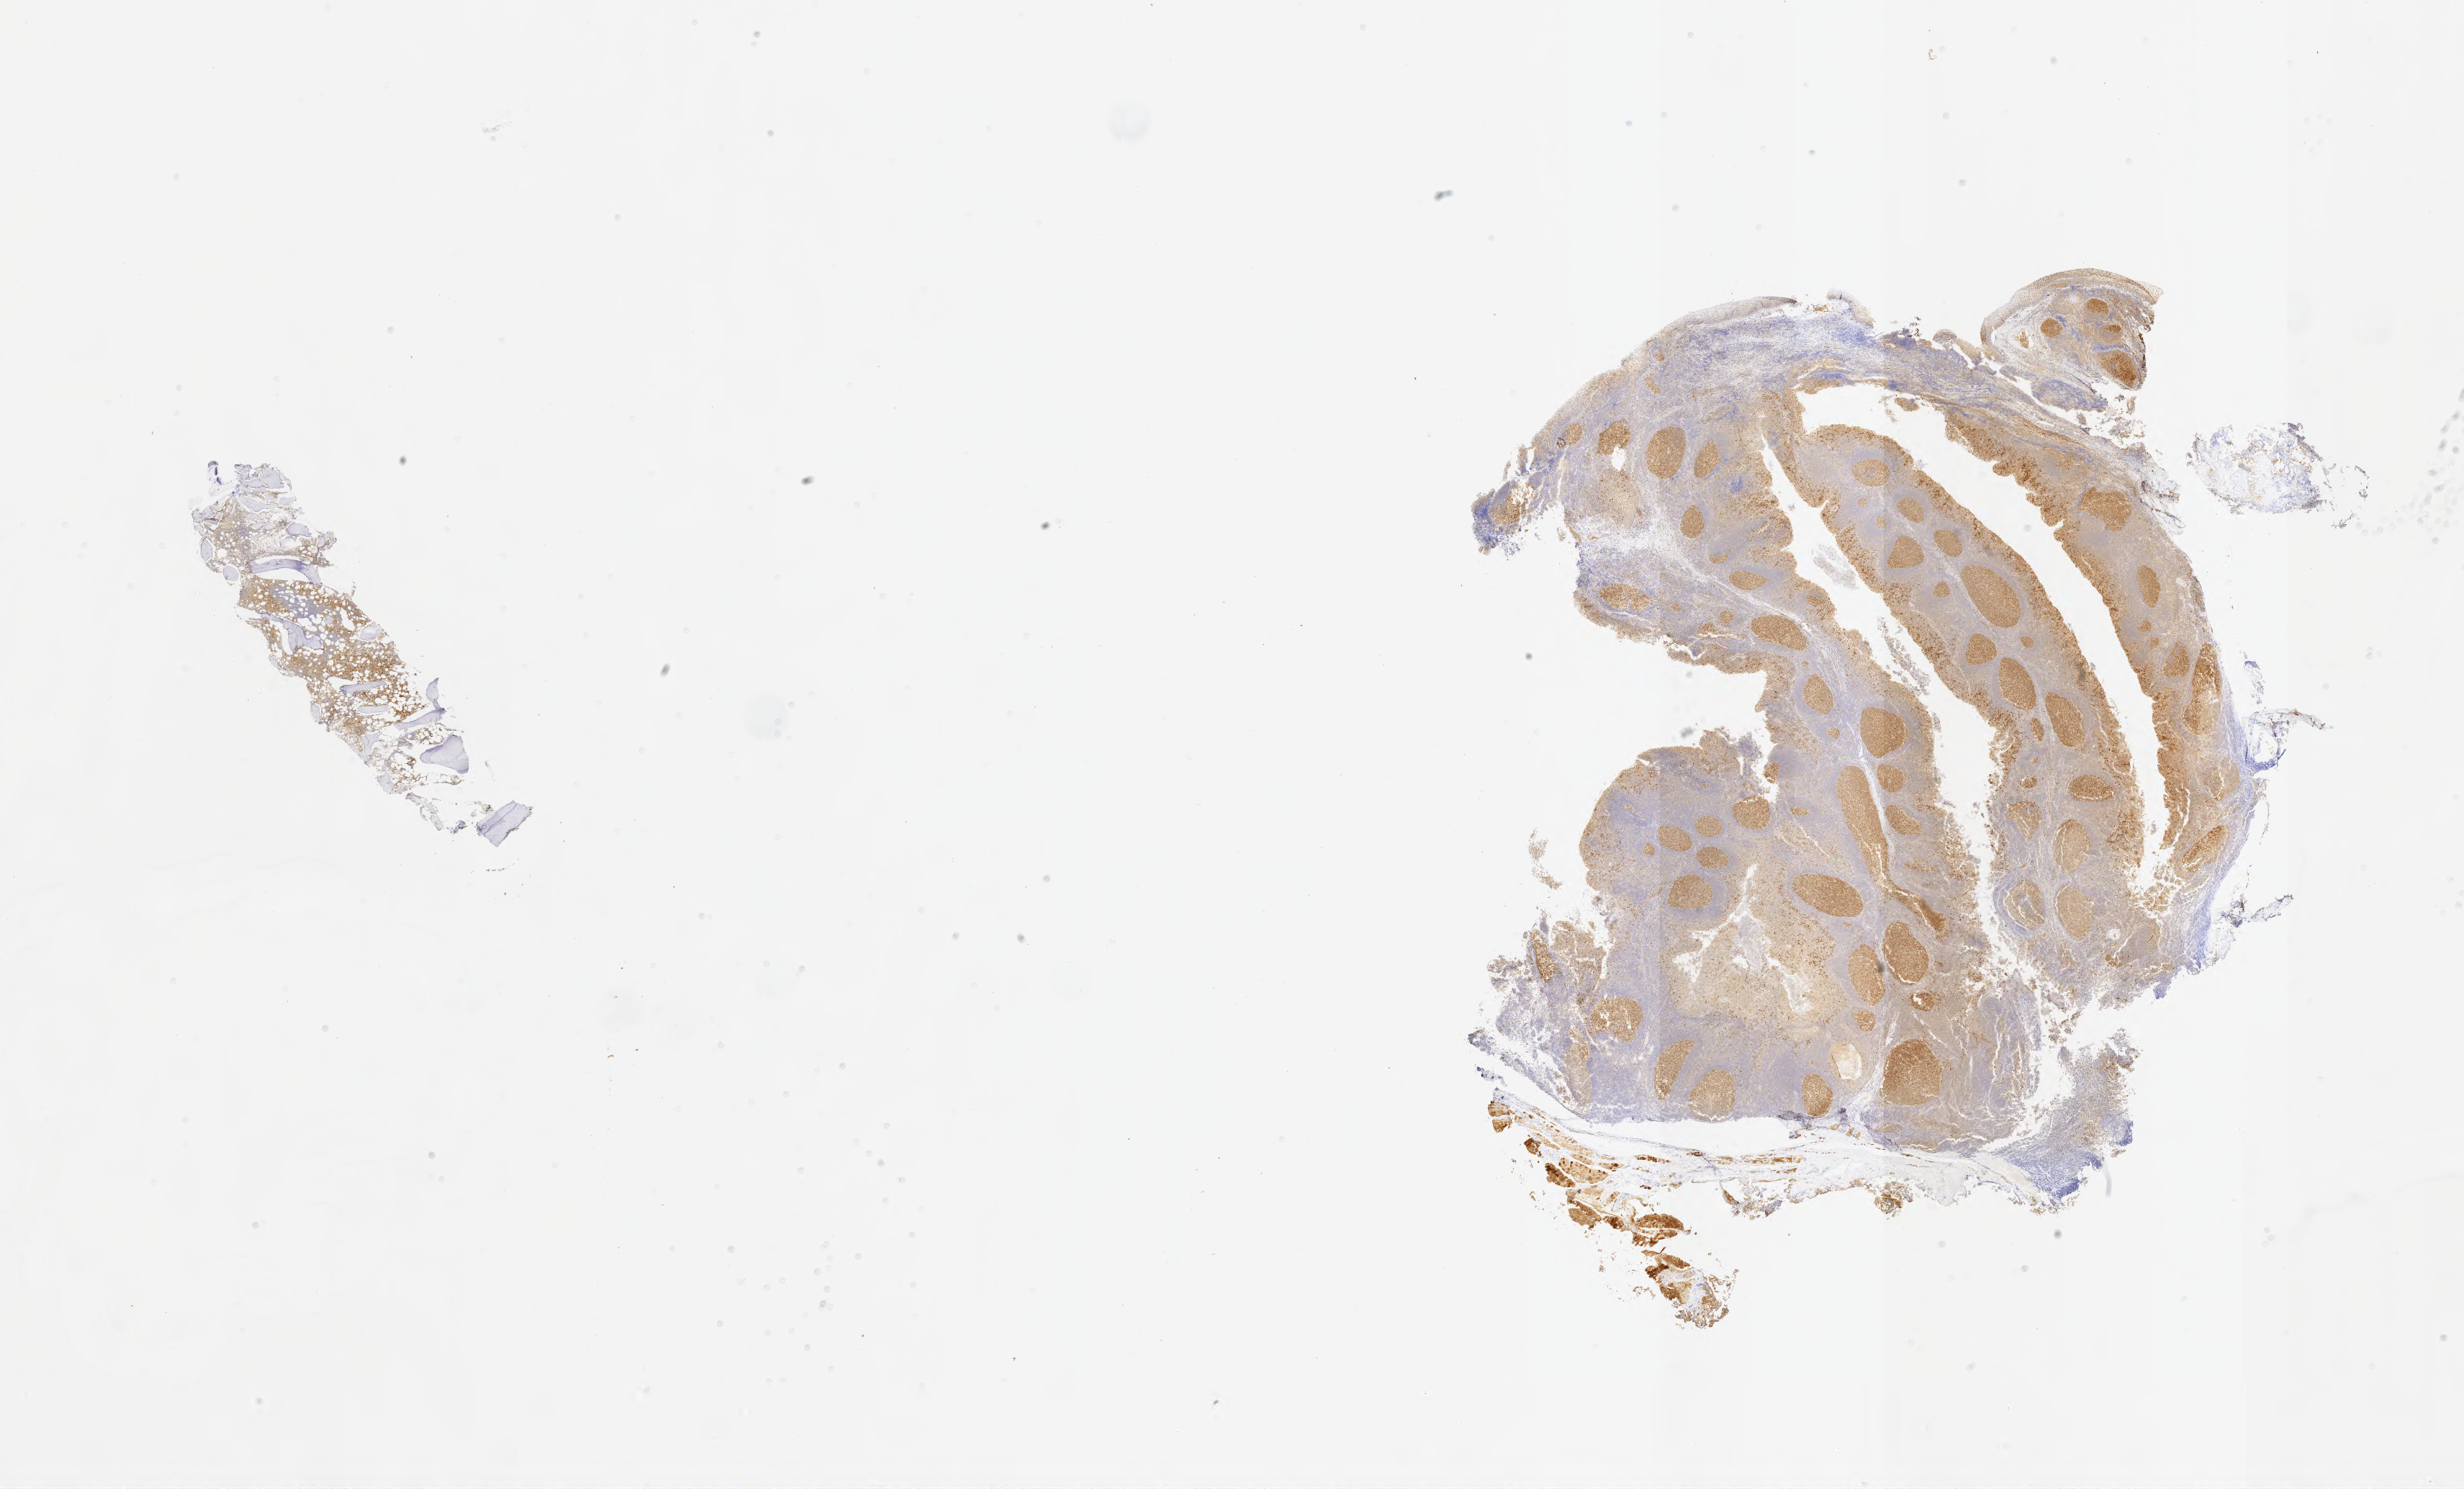
Whole-slide image, immunohistochemical stain for BCL6 — a low-resolution overview of the entire scanned area, about 27.7 x 16.7 mm; specimen: tumor tissue; anatomic site: bone marrow. Female, age 4 years at initial diagnosis.
* histologic diagnosis: Burkitt lymphoma, NOS